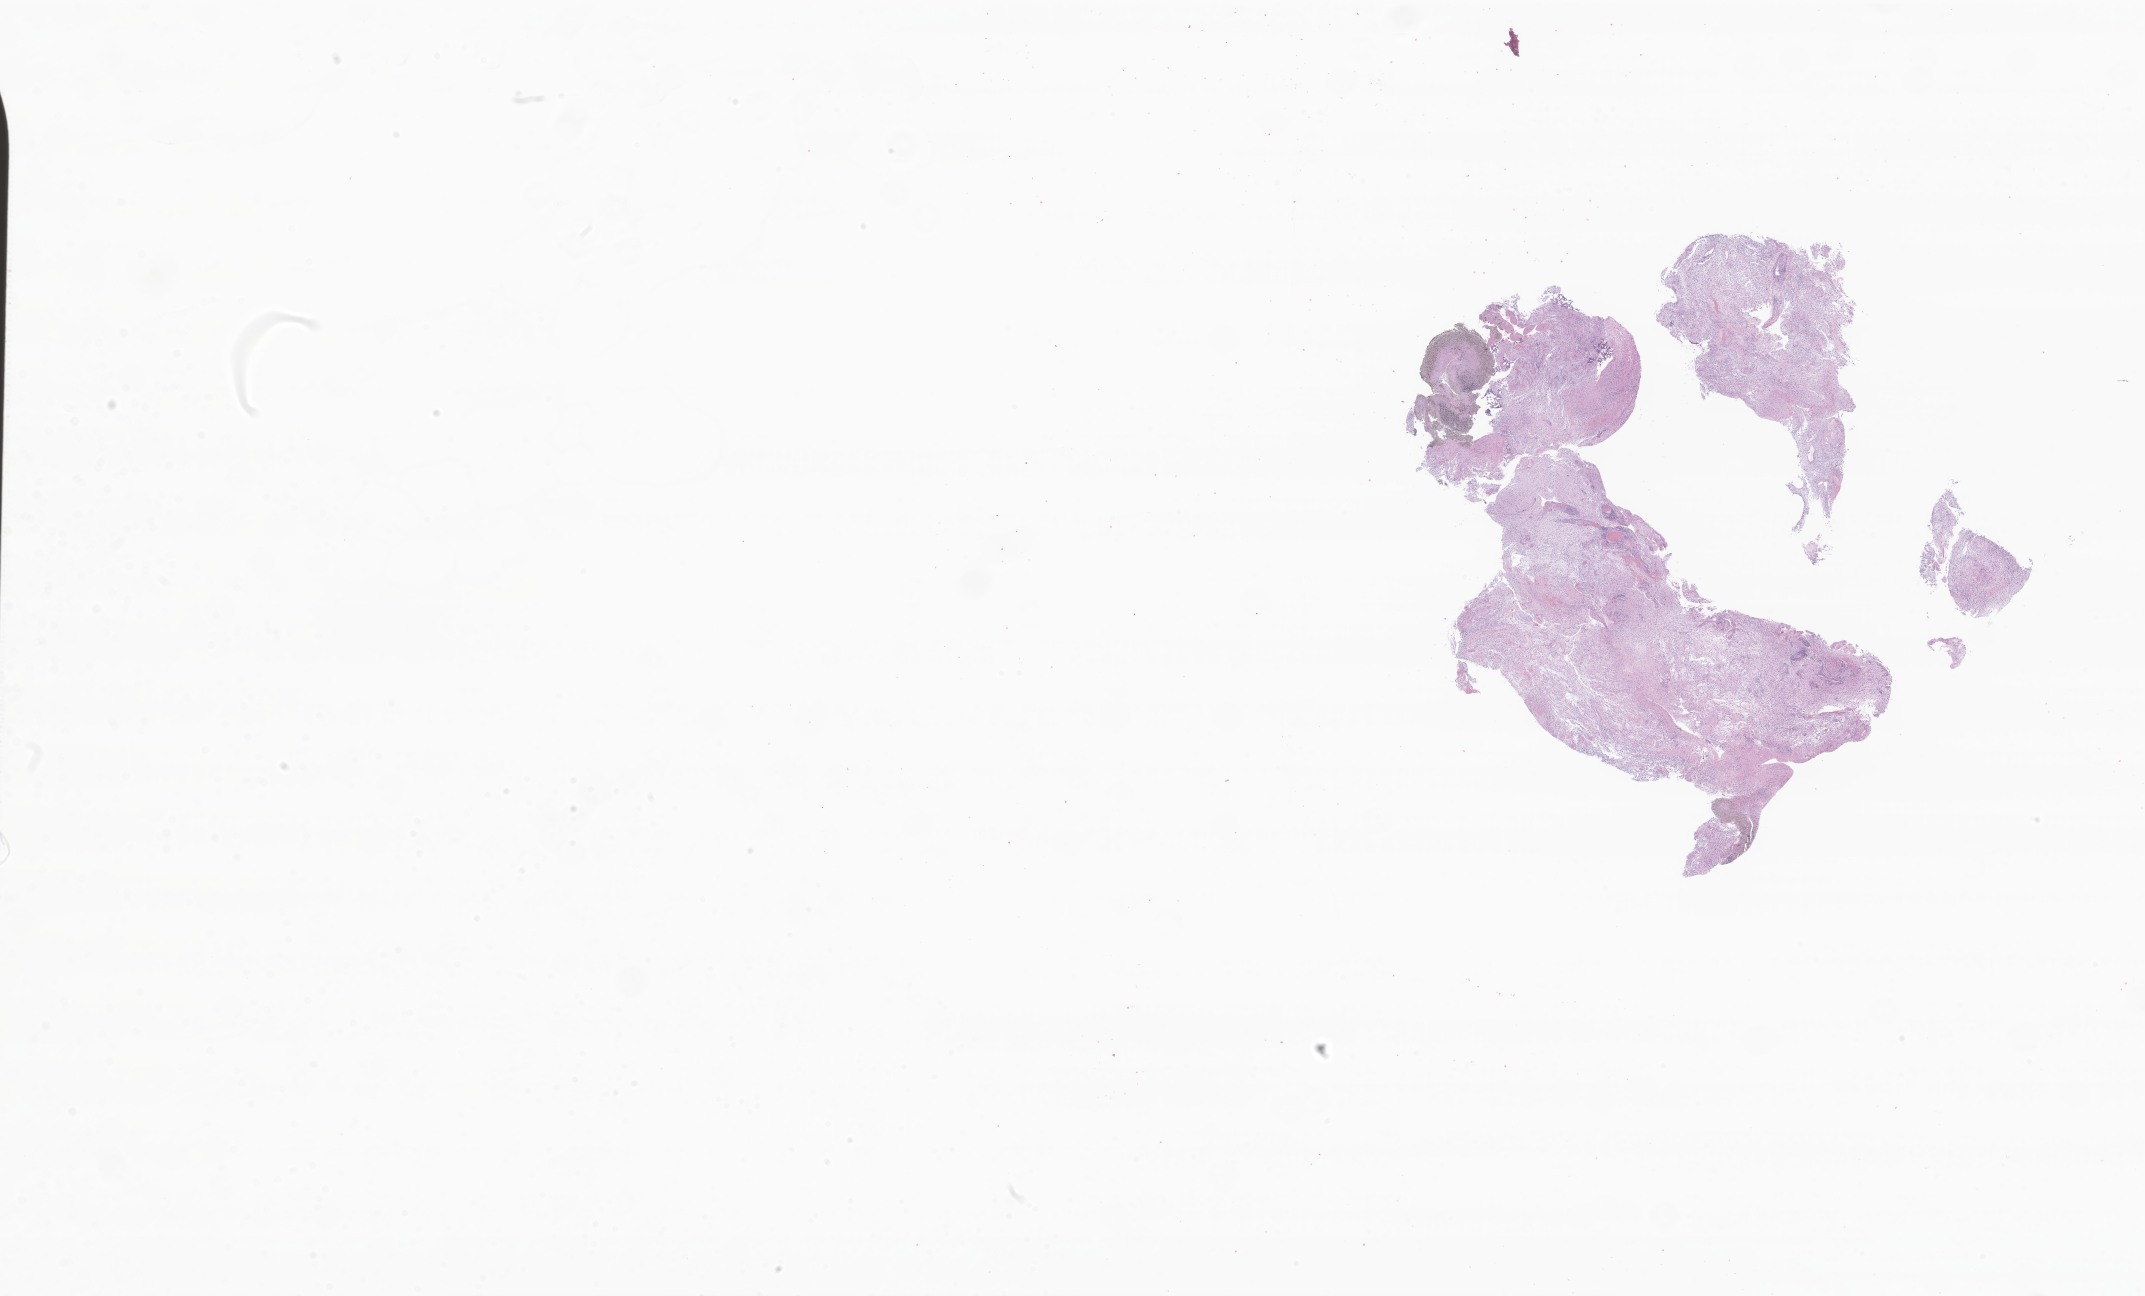
Digitized H&E-stained section of tumor tissue from the brain, a low-resolution overview of the entire scanned area, about 36.2 x 21.9 mm, formalin-fixed, paraffin-embedded (FFPE) tissue. Patient: male, age 124 months.
Diagnosis (ICD-O-3 morphology term): Pilocytic astrocytoma.